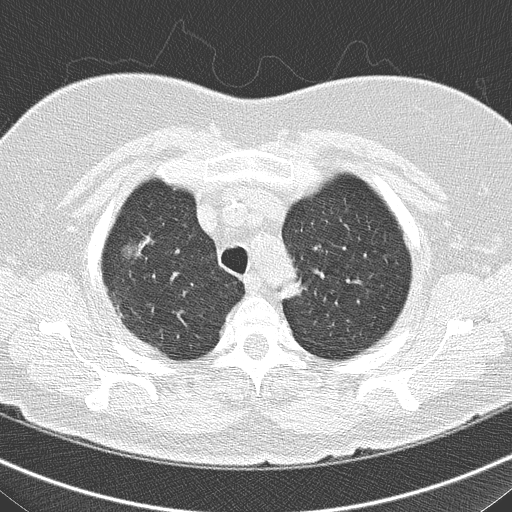
Chest CT (low-dose screening protocol), one axial image. Third annual screen. Lung window (W 1500 / L -600 HU). Lung (sharp) reconstruction kernel (B50f). 120 kVp. 512 × 512 image matrix, field of view 316 × 316 mm. Female participant, aged 74 years at enrolment. Former smoker at enrolment.
Expert reader's lesion annotation, bounding box (x1, y1, x2, y2) in pixels: (110, 228, 177, 294). The screening reader recorded 5 non-calcified nodules or masses ≥4 mm on this exam (right upper lobe, right middle lobe, right middle lobe, left lower lobe, right lower lobe); which of them this box marks is not recorded. Lung cancer was diagnosed 117 days after this screen: bronchiolo-alveolar carcinoma, non-mucinous, right upper lobe, well differentiated (G1), stage IA (AJCC 6th edition), 14 mm at pathology.